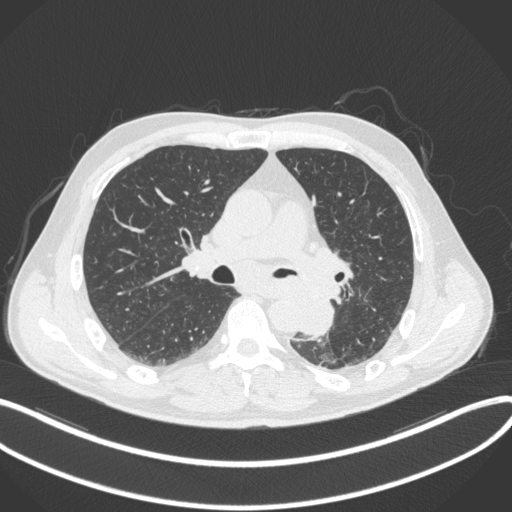
Chest CT, one axial slice; position 202 of 328 along the scan axis; lung window (W 1500 / L -600 HU); 512 × 512 image matrix, field of view 400 × 400 mm. Male patient, age 59 years. From the clinical record (not read from this slice): clinical TNM (as recorded): T2a N2 M0.
Outlined on this slice (bounding box drawn by a radiologist):
- lung tumour (recorded histology: squamous cell carcinoma): bounding box <294,286,338,342> (left, top, right, bottom; pixels)